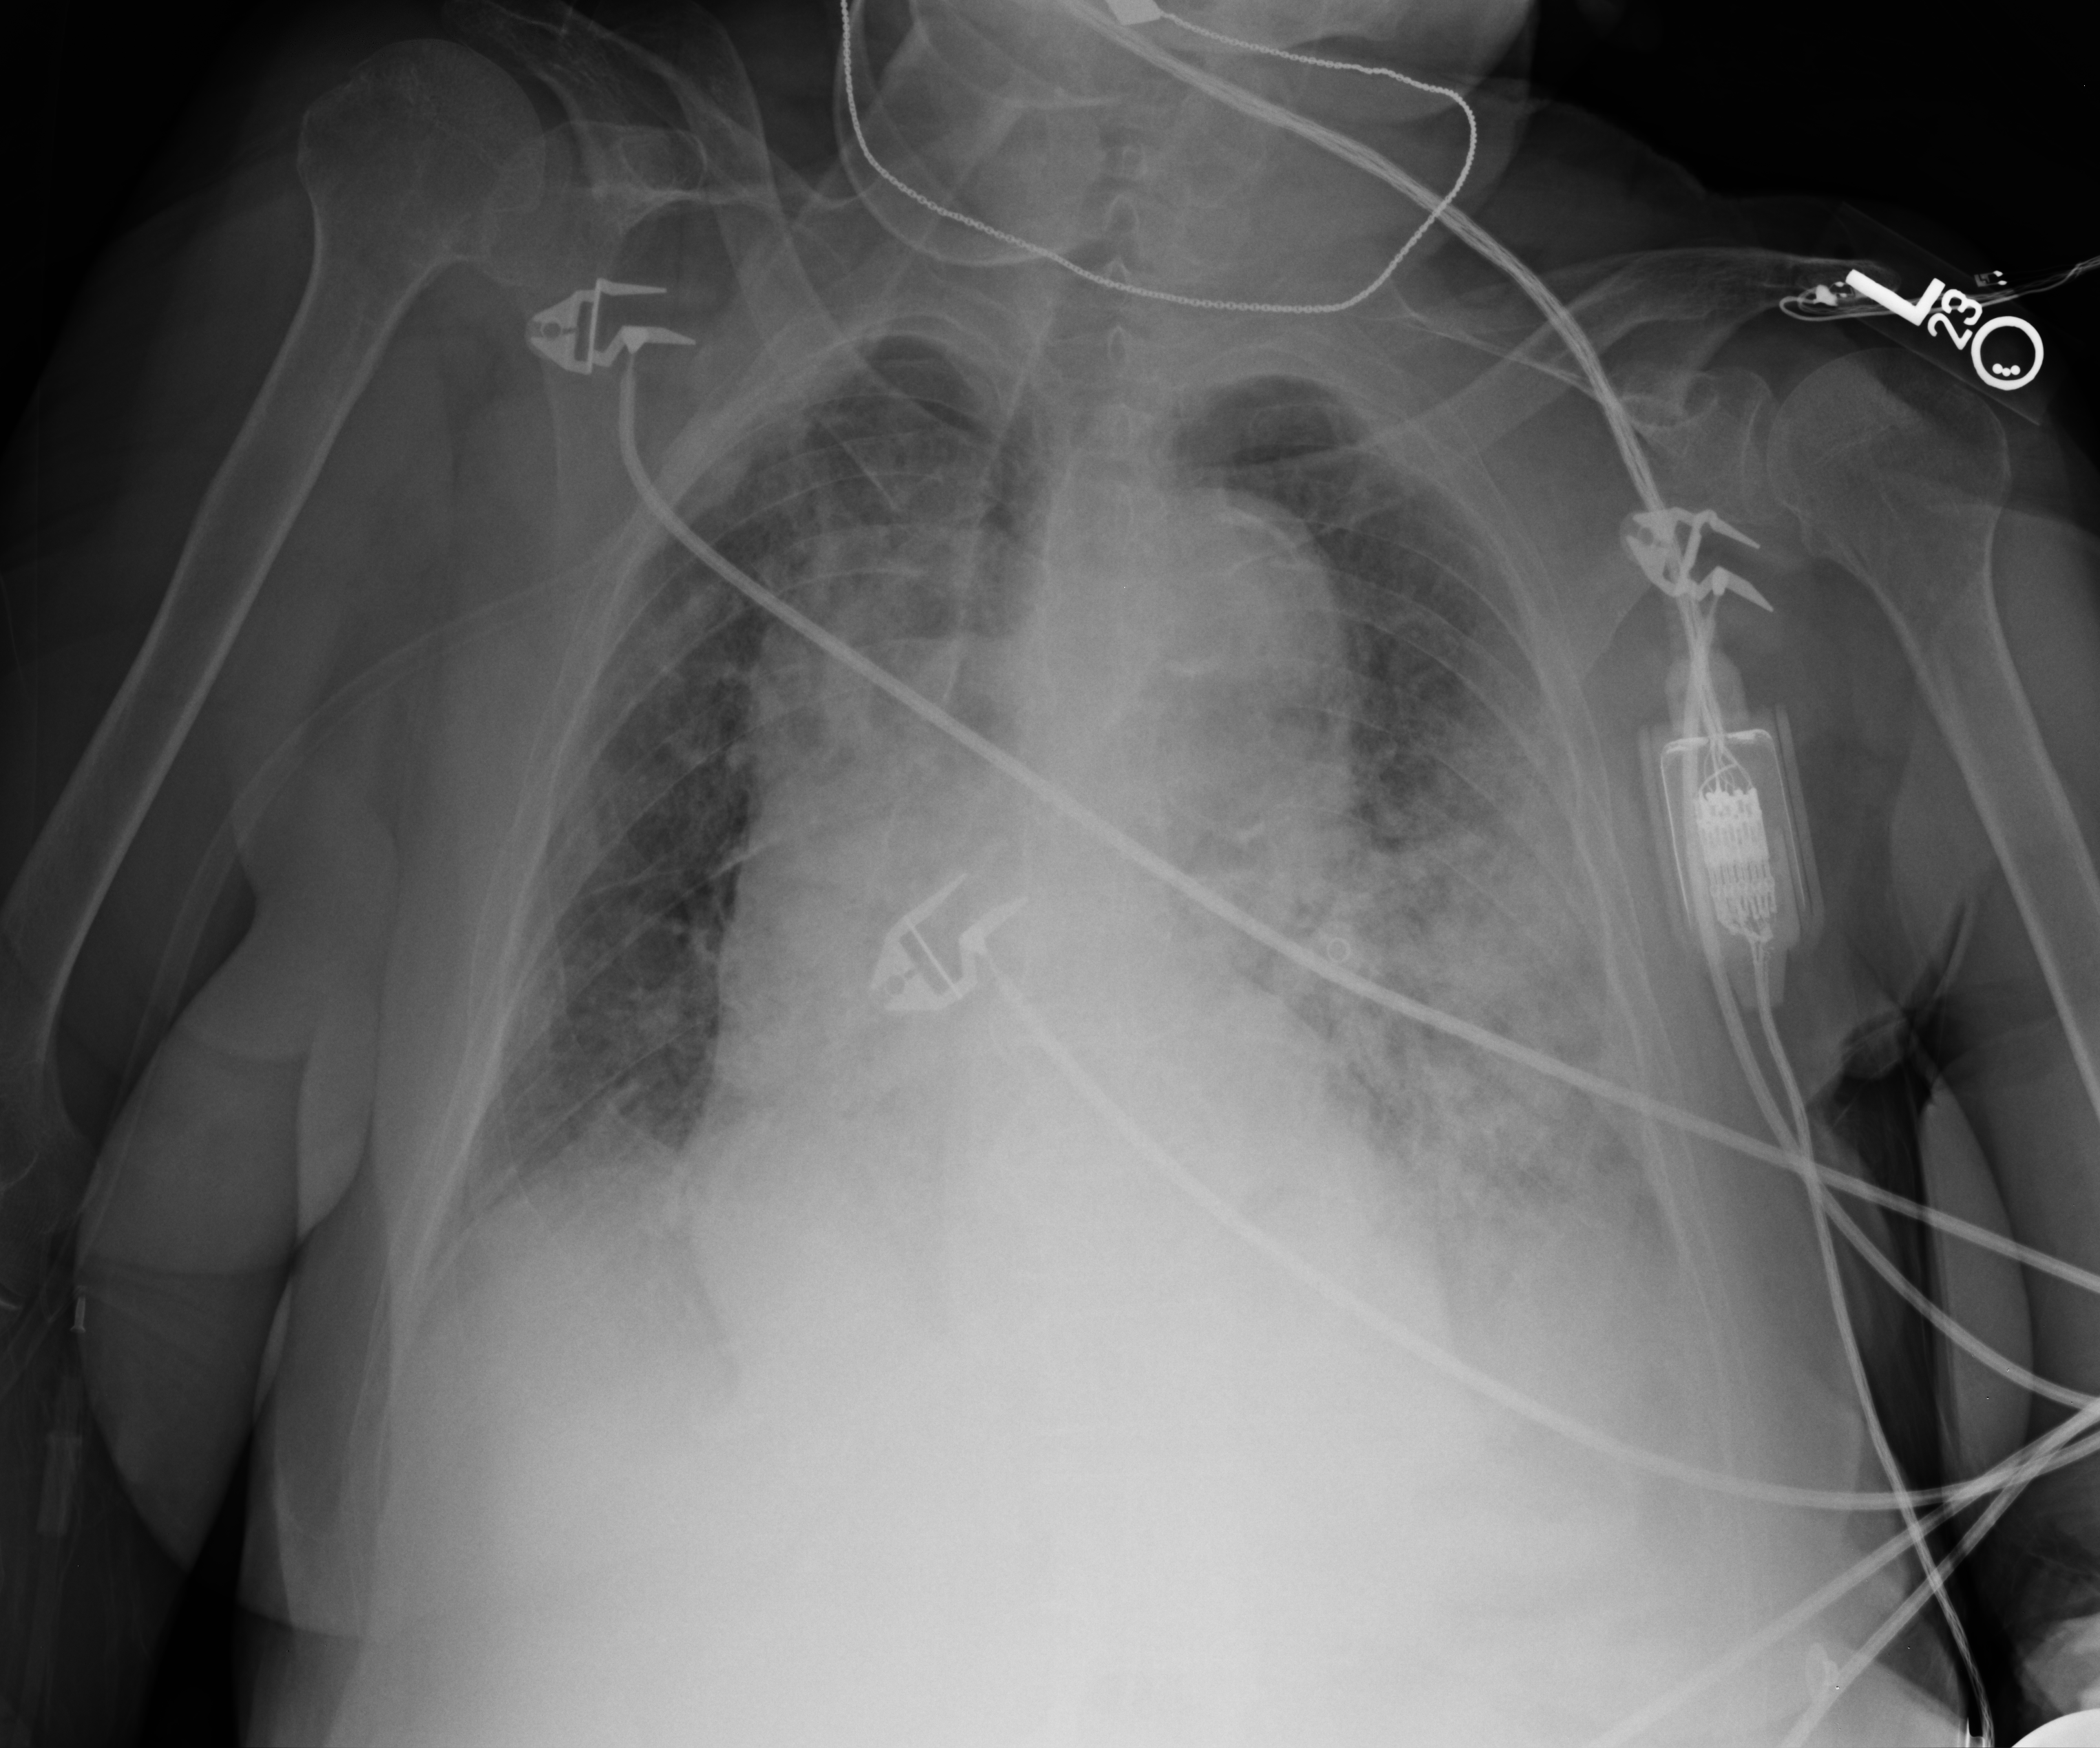
Bedside chest radiograph (computed radiography); anteroposterior (AP) projection. Female patient hospitalised with COVID-19, age 75–90 years.
Admission-level facts for this patient (not findings on this image; timing relative to this image not recorded): mechanically ventilated during this hospital stay: no; admitted to intensive care during this hospital stay: no.